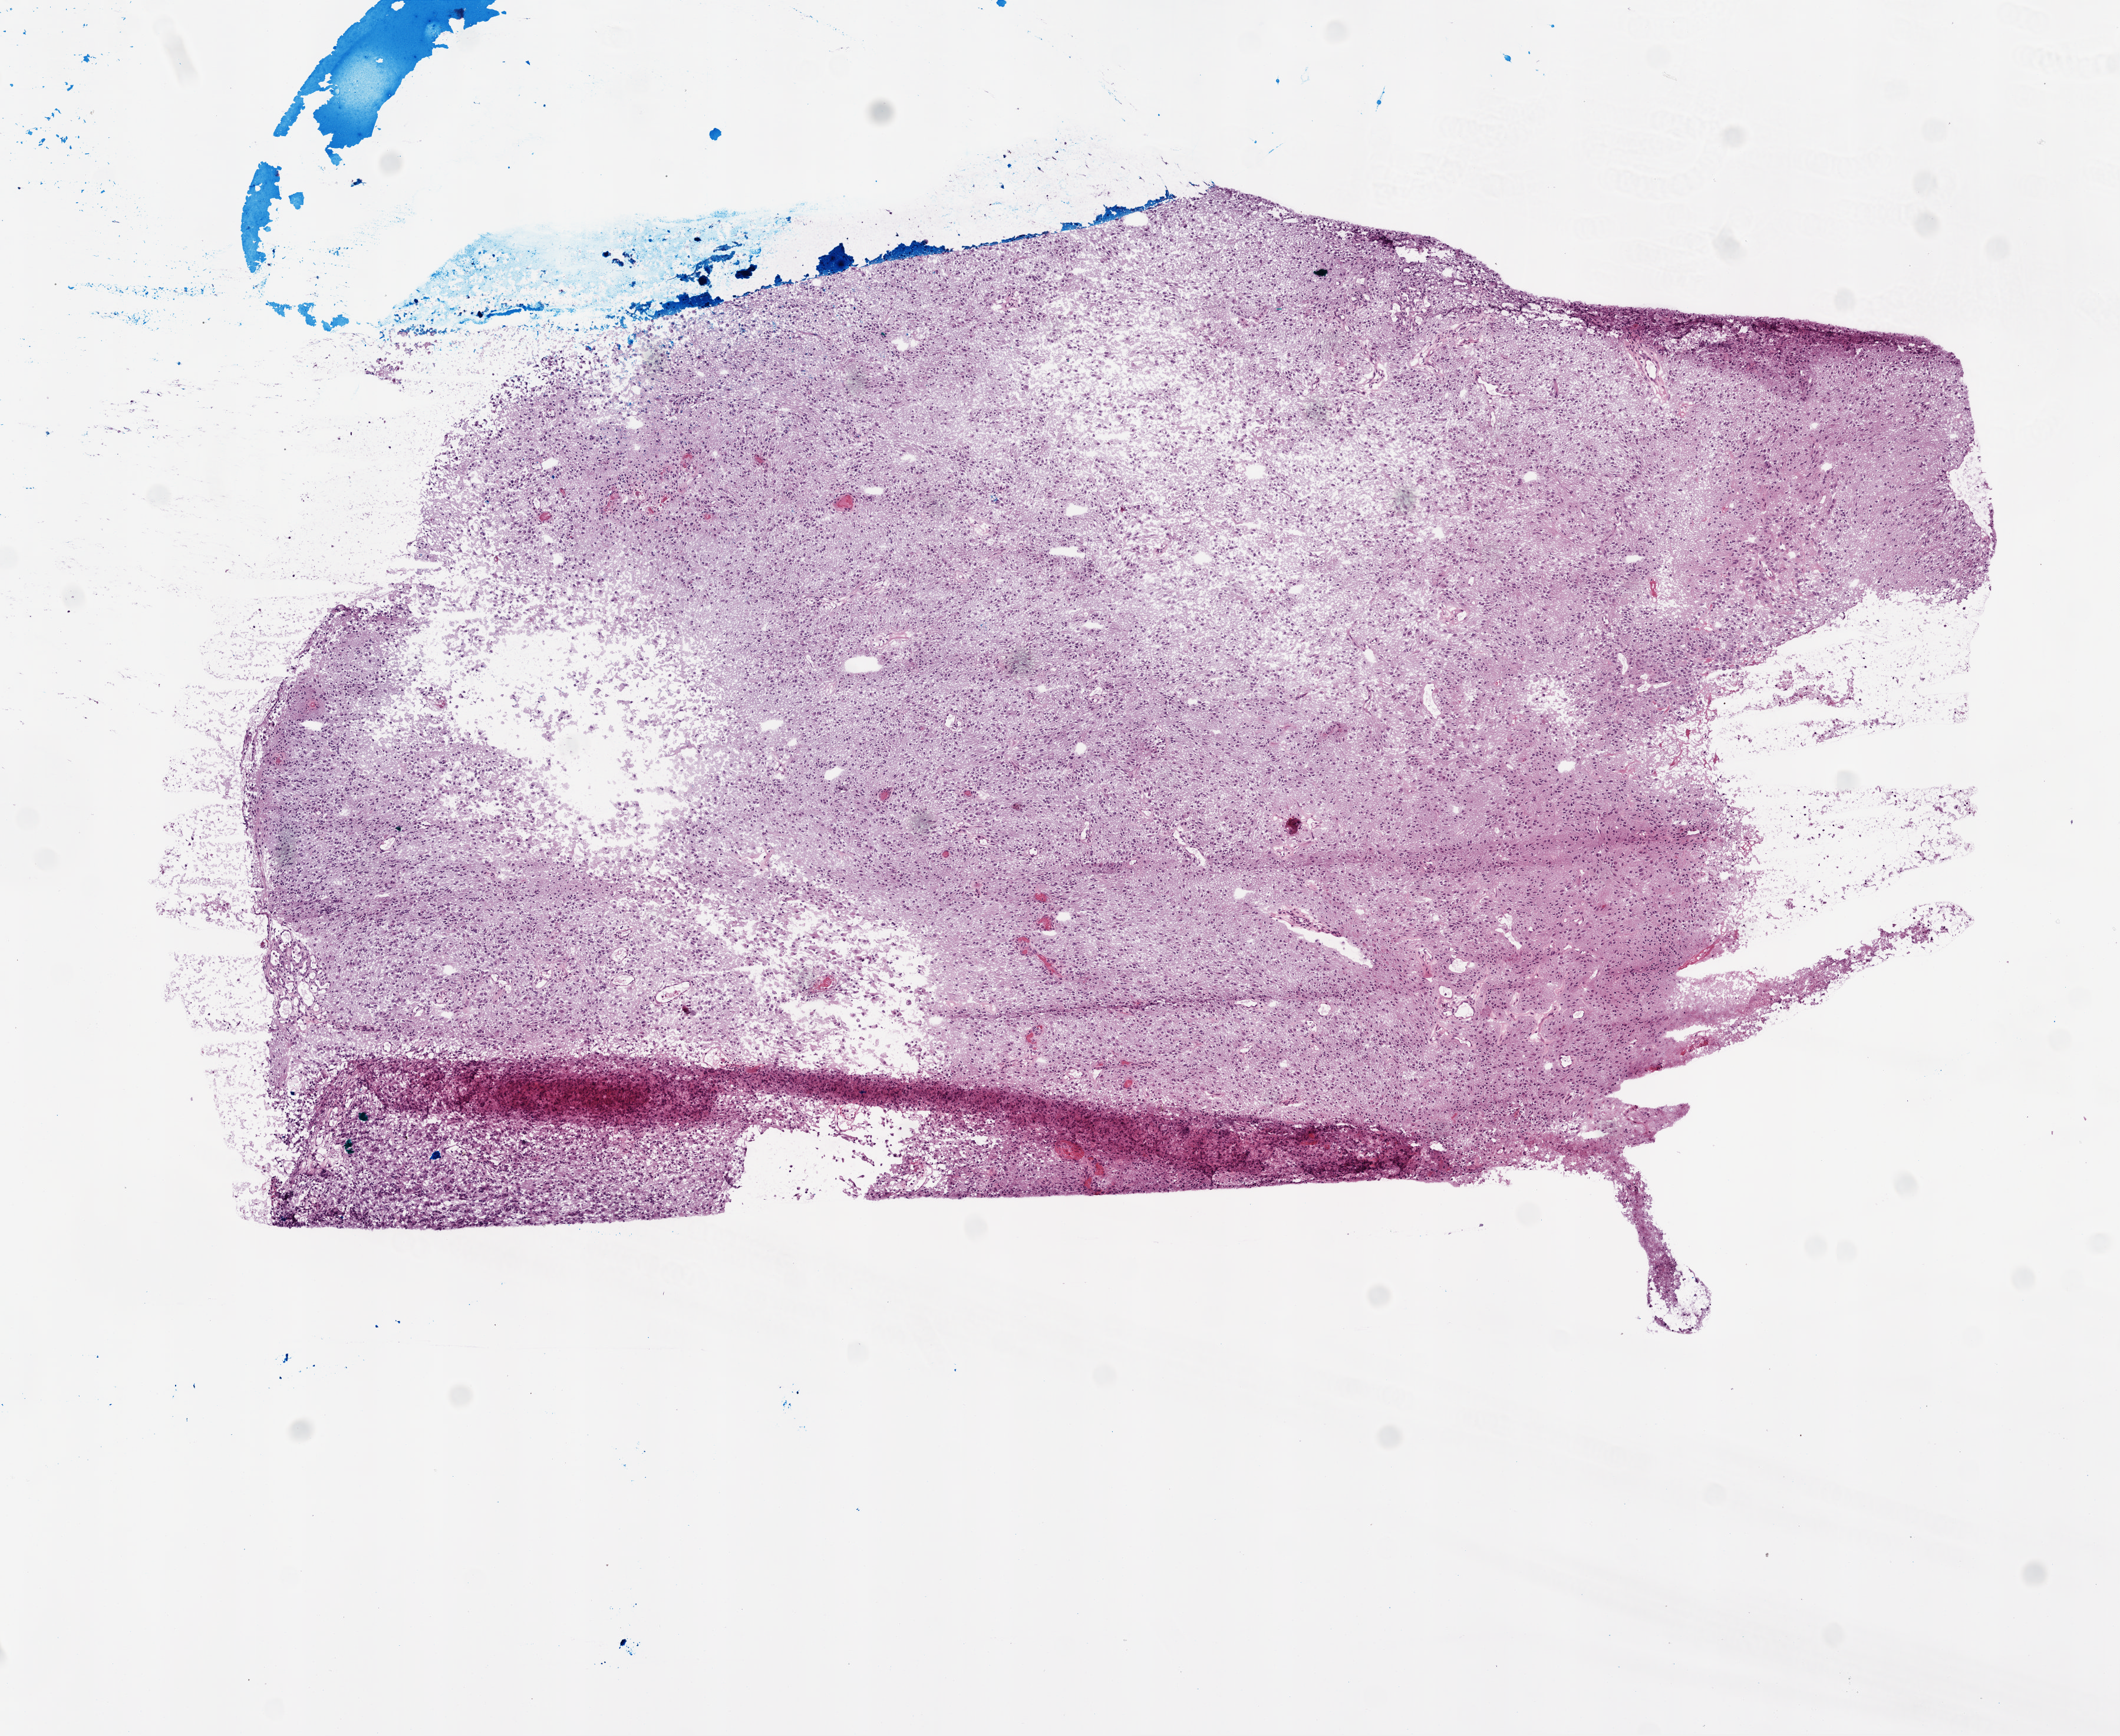
Whole-slide histology image, H&E-stained — low-resolution overview of the scanned area, about 7.3 x 5.9 mm (from a 20x scan); frozen section; primary tumour sample from the brain. Male, age 70 years at initial diagnosis. Slide review estimates, as recorded: tumour cells 80%, tumour nuclei 90%, normal cells 0%, stromal cells 10%, necrosis 10%.
Diagnosis: Glioblastoma.